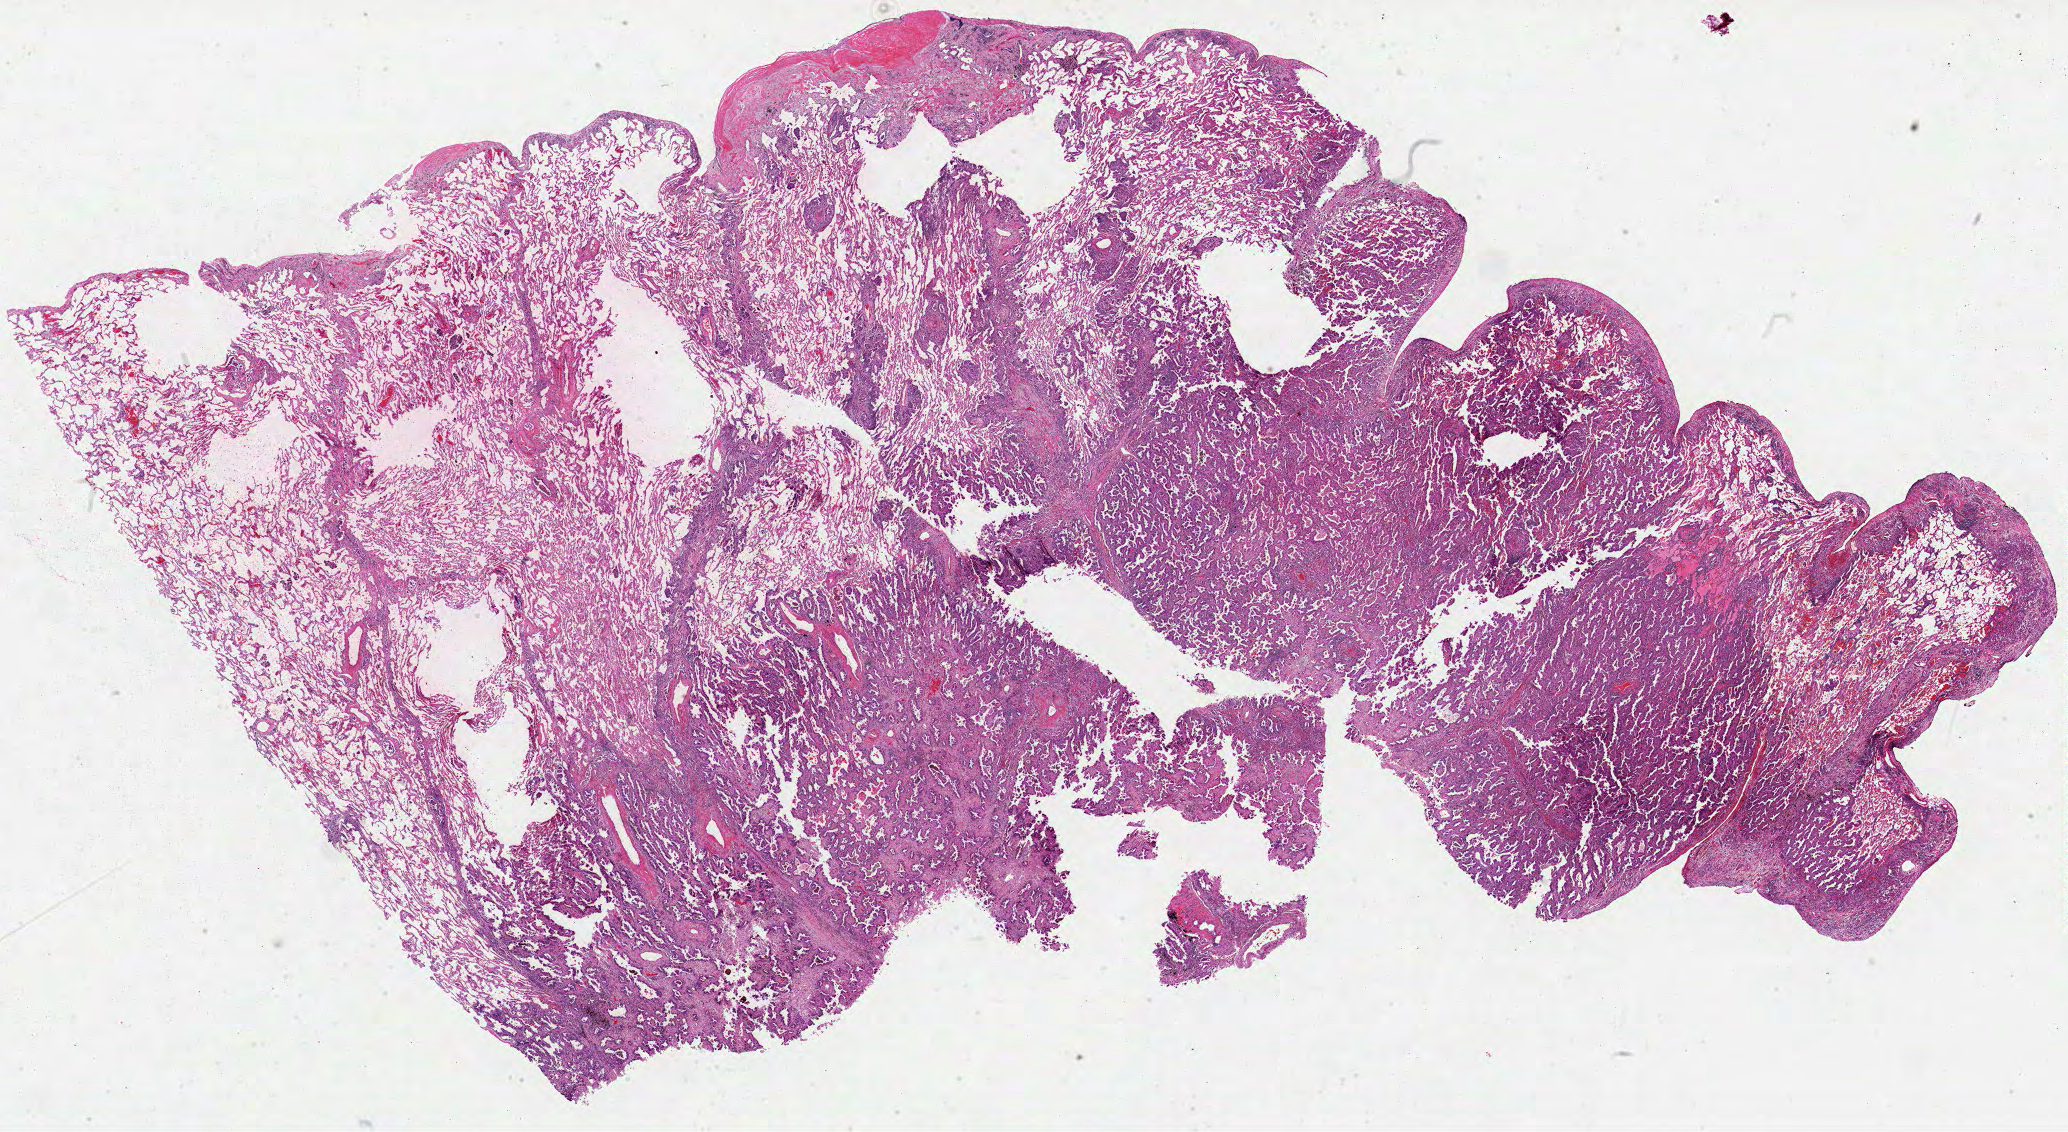
Digitized Hematoxylin and eosin (H&E) stained tissue section (whole slide), a low-resolution overview of the entire scanned area, about 33.4 x 18.3 mm (slide scanned at 40x); FFPE section; primary tumour sample from the lung. Female patient; age at initial diagnosis 45 years.
AJCC pathologic stage: IIIA (4th edition). Diagnosis: Adenocarcinoma, NOS (upper lobe, lung).